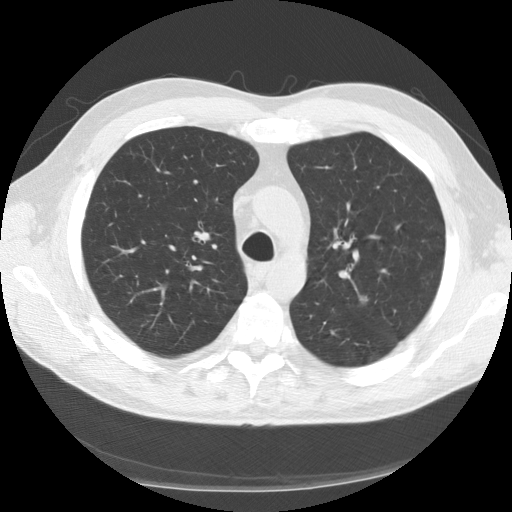
Chest CT (low-dose screening protocol), one axial image. Second annual screen. Lung window (W 1500 / L -600 HU). Slice 41 of 152 in the series. Male participant, aged 57 years at enrolment. Current smoker at enrolment.
- Lesion marked by an expert reader, bounding box (x1, y1, x2, y2) in pixels: (342, 282, 382, 327).
- The exam's reader record, not a measurement of the box and not confirmed to be the same lesion: non-calcified nodule or mass ≥4 mm, left upper lobe, 12 × 7 mm, spiculated (stellate) margins, mixed attenuation, pre-existing on the prior screen: no.
- Official screen result: positive, other.
- Participant outcome: lung cancer diagnosed 419 days after this screen — adenosquamous carcinoma, left upper lobe, poorly differentiated (G3), stage IA (AJCC 6th edition), 15 mm at pathology.